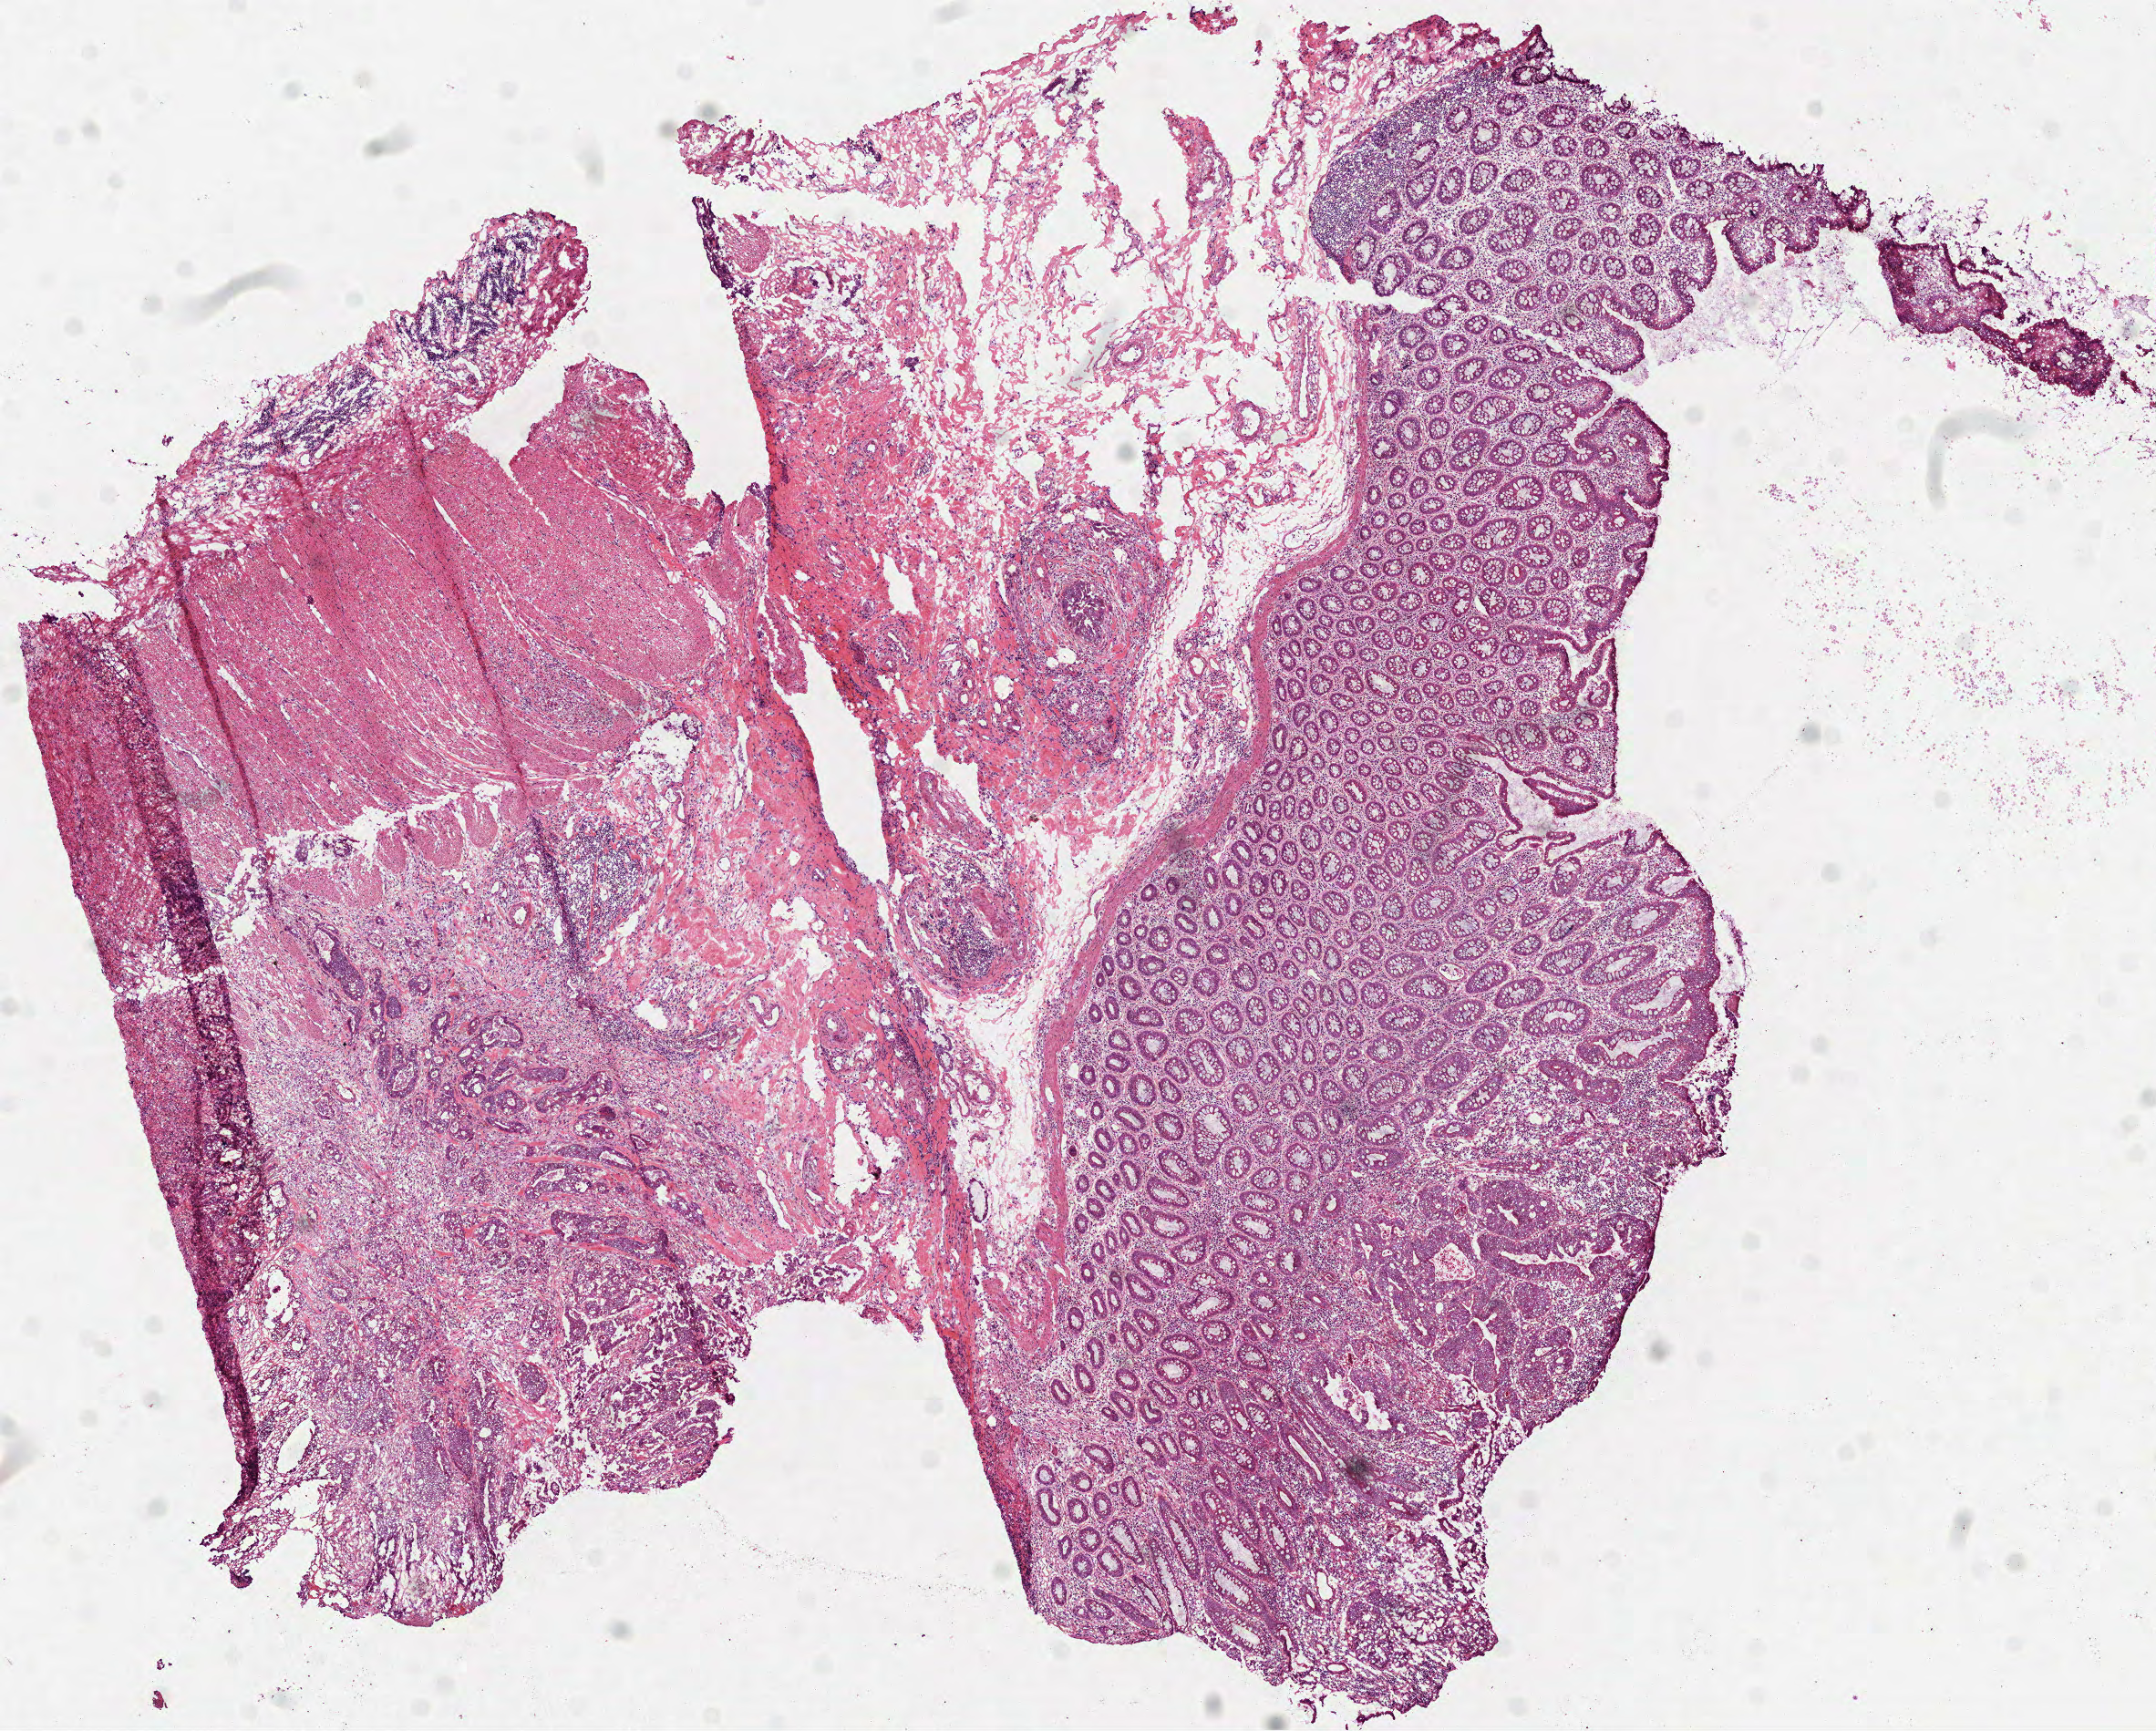
Whole-slide histology image, H&E-stained, whole scanned area (about 9.5 x 7.7 mm) shown as a low-resolution overview; frozen section; sample: primary tumour, colon. Patient sex: male. Pathologist review of this section (percent, as recorded): tumour cells 18%, tumour nuclei 15%, normal cells 40%, stromal cells 40%, necrosis 2%.
Diagnosis: Adenocarcinoma, NOS. AJCC pathologic stage: IIA.